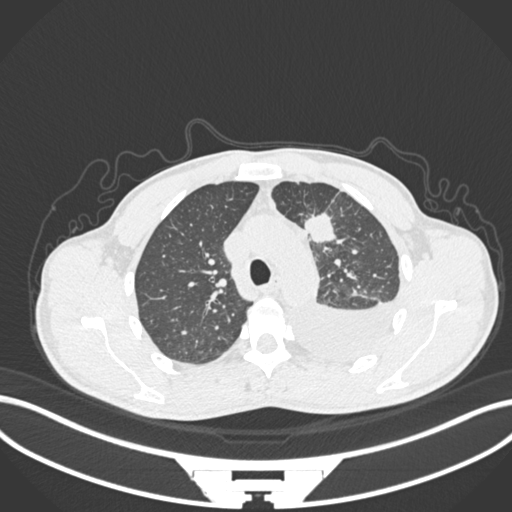
Chest CT, one axial slice. Slice 160 of 244 in the series (ordered by position). Reconstruction kernel B30f. 120 kVp. Lung window (W 1500 / L -600 HU). 1 mm slice thickness. 512 × 512 image matrix, field of view 400 × 400 mm. Male patient, age 49 years. Case-level facts recorded for this patient, not image findings: clinical TNM (as recorded): T1c N1 M1.
Structures marked on this image (bounding box drawn by a radiologist):
- lung tumour (recorded histology: adenocarcinoma): box from (x=305, y=212) to (x=337, y=248) px